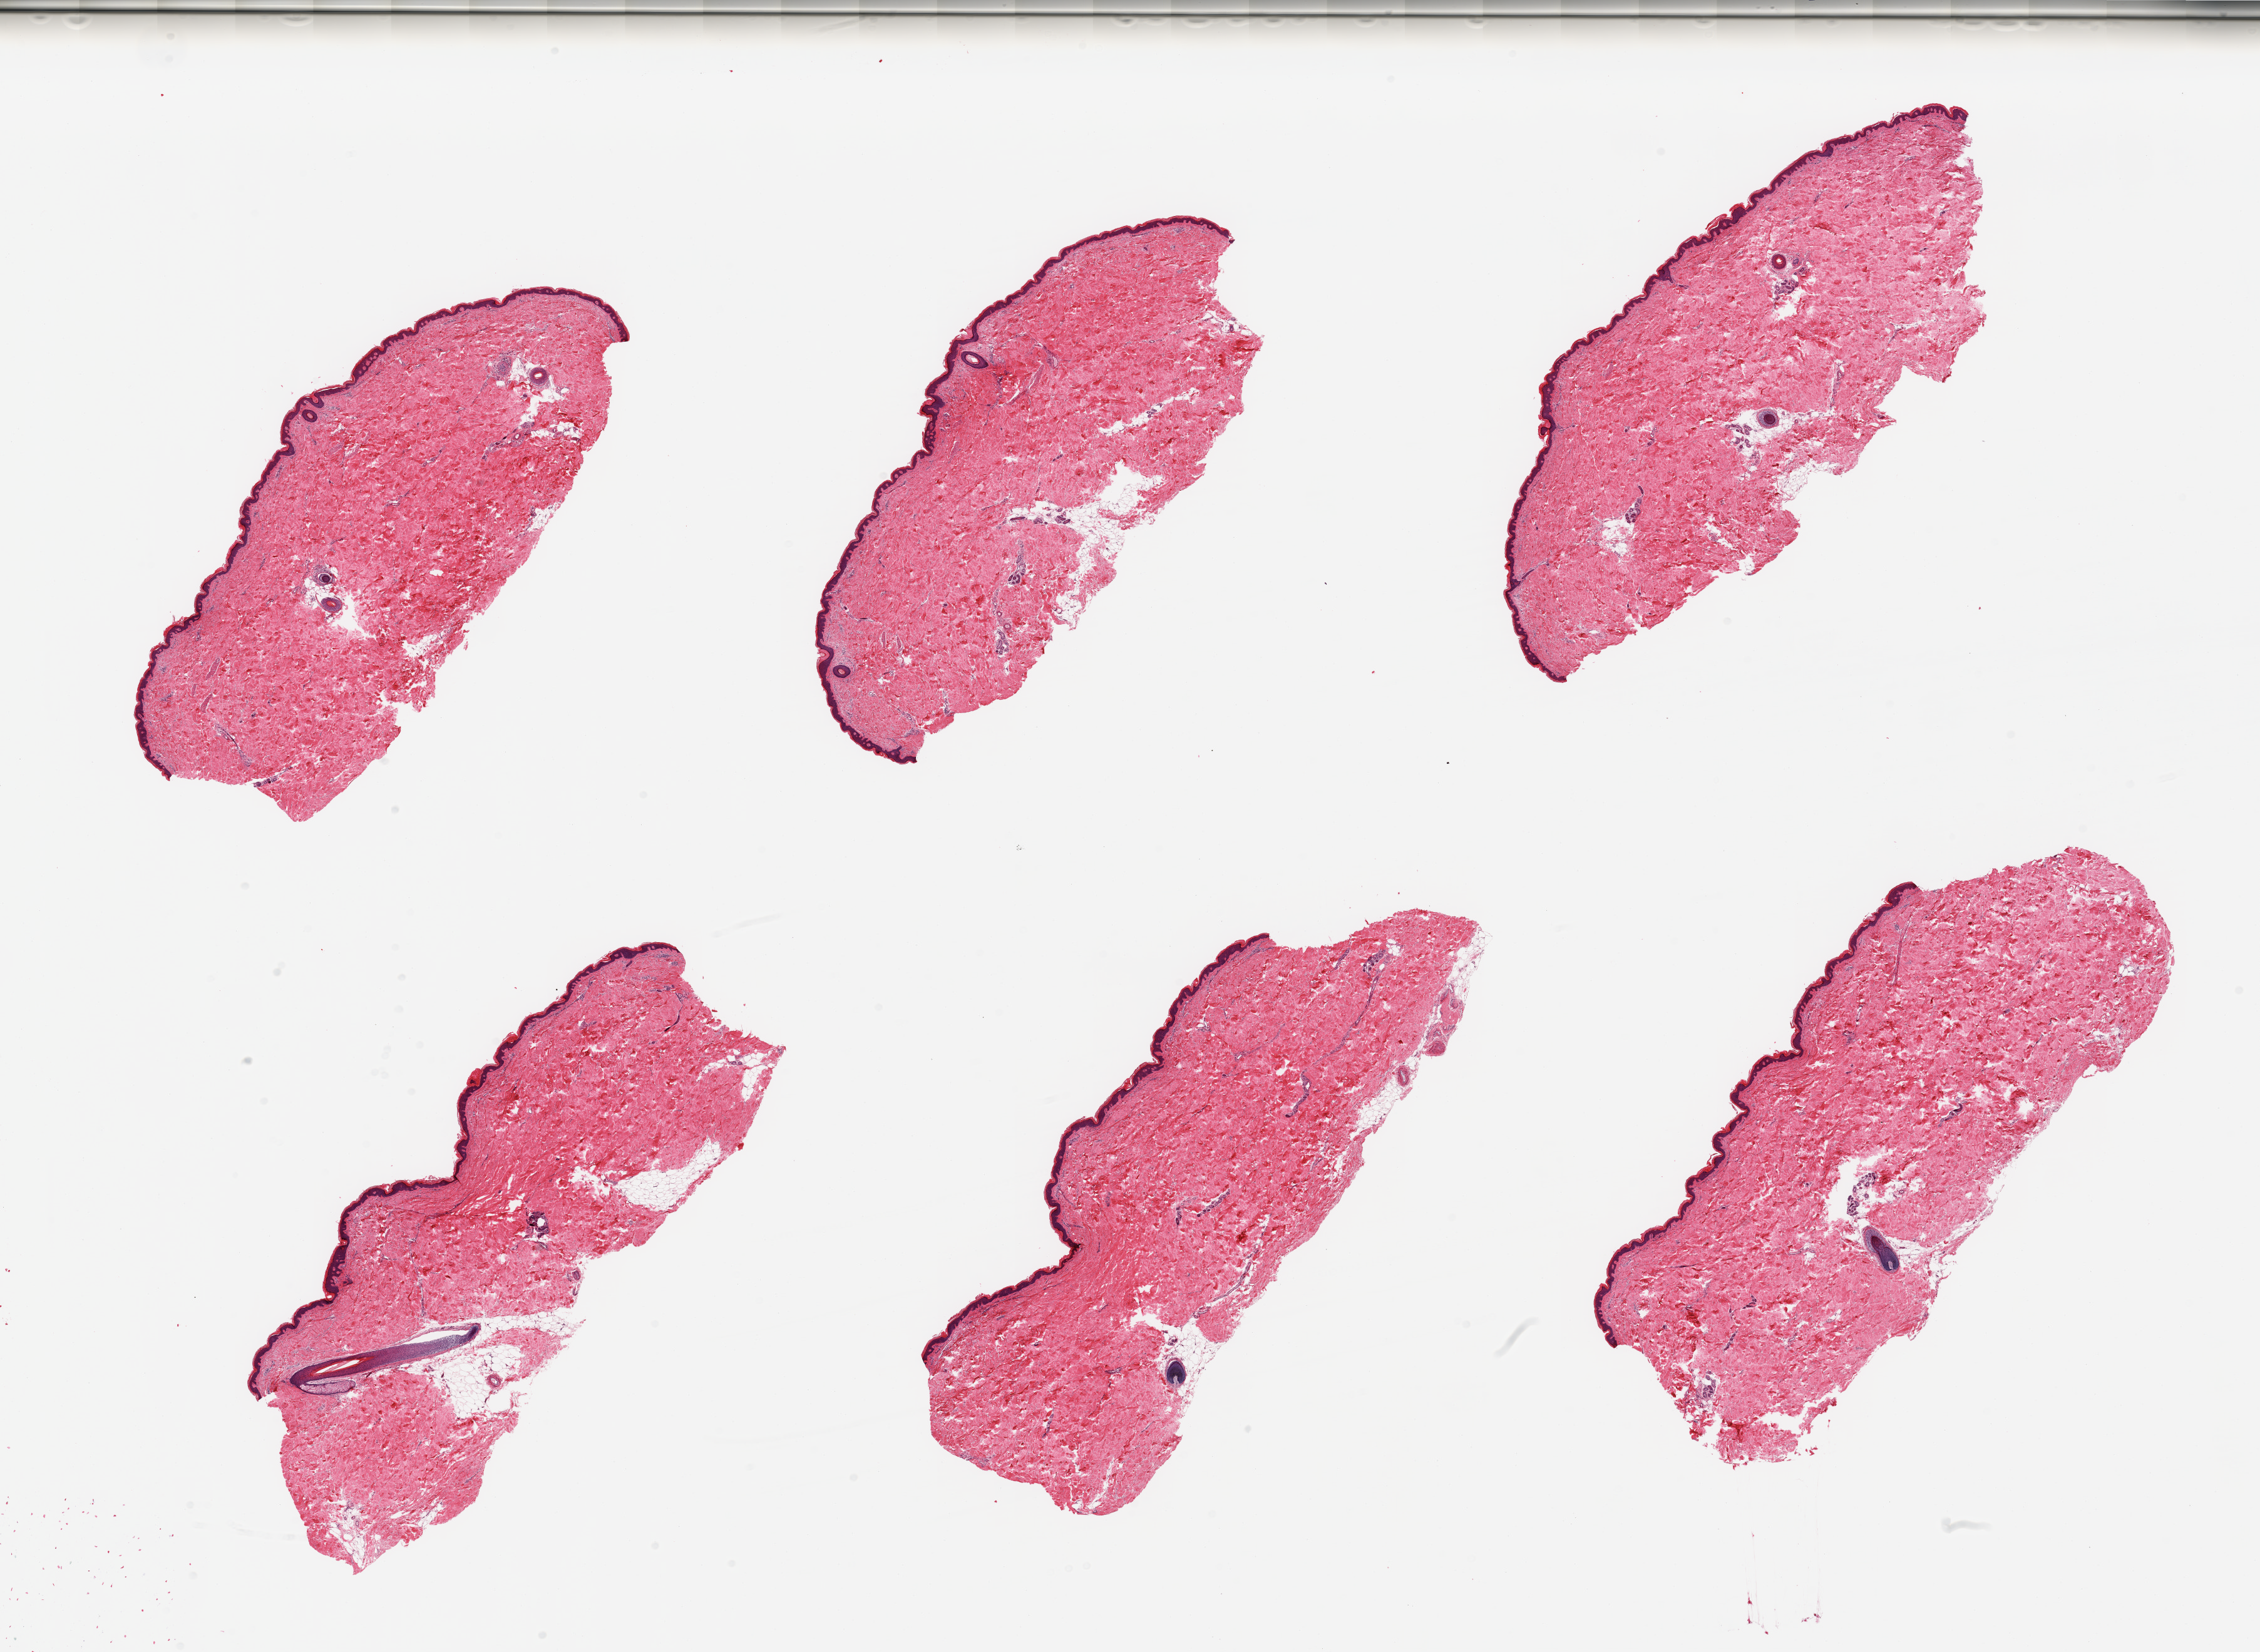
Whole-slide image, H&E stain — a low-resolution overview of the entire scanned area, about 28.5 x 20.9 mm. PAXgene-fixed paraffin-embedded (PFPE) section. Target tissue: skin of lower leg. Tissue donor sample.
Reviewer comment on this tissue sample: 6 pieces; <10% dermal fat; ~50 microns thick epidermis; well trimmed.